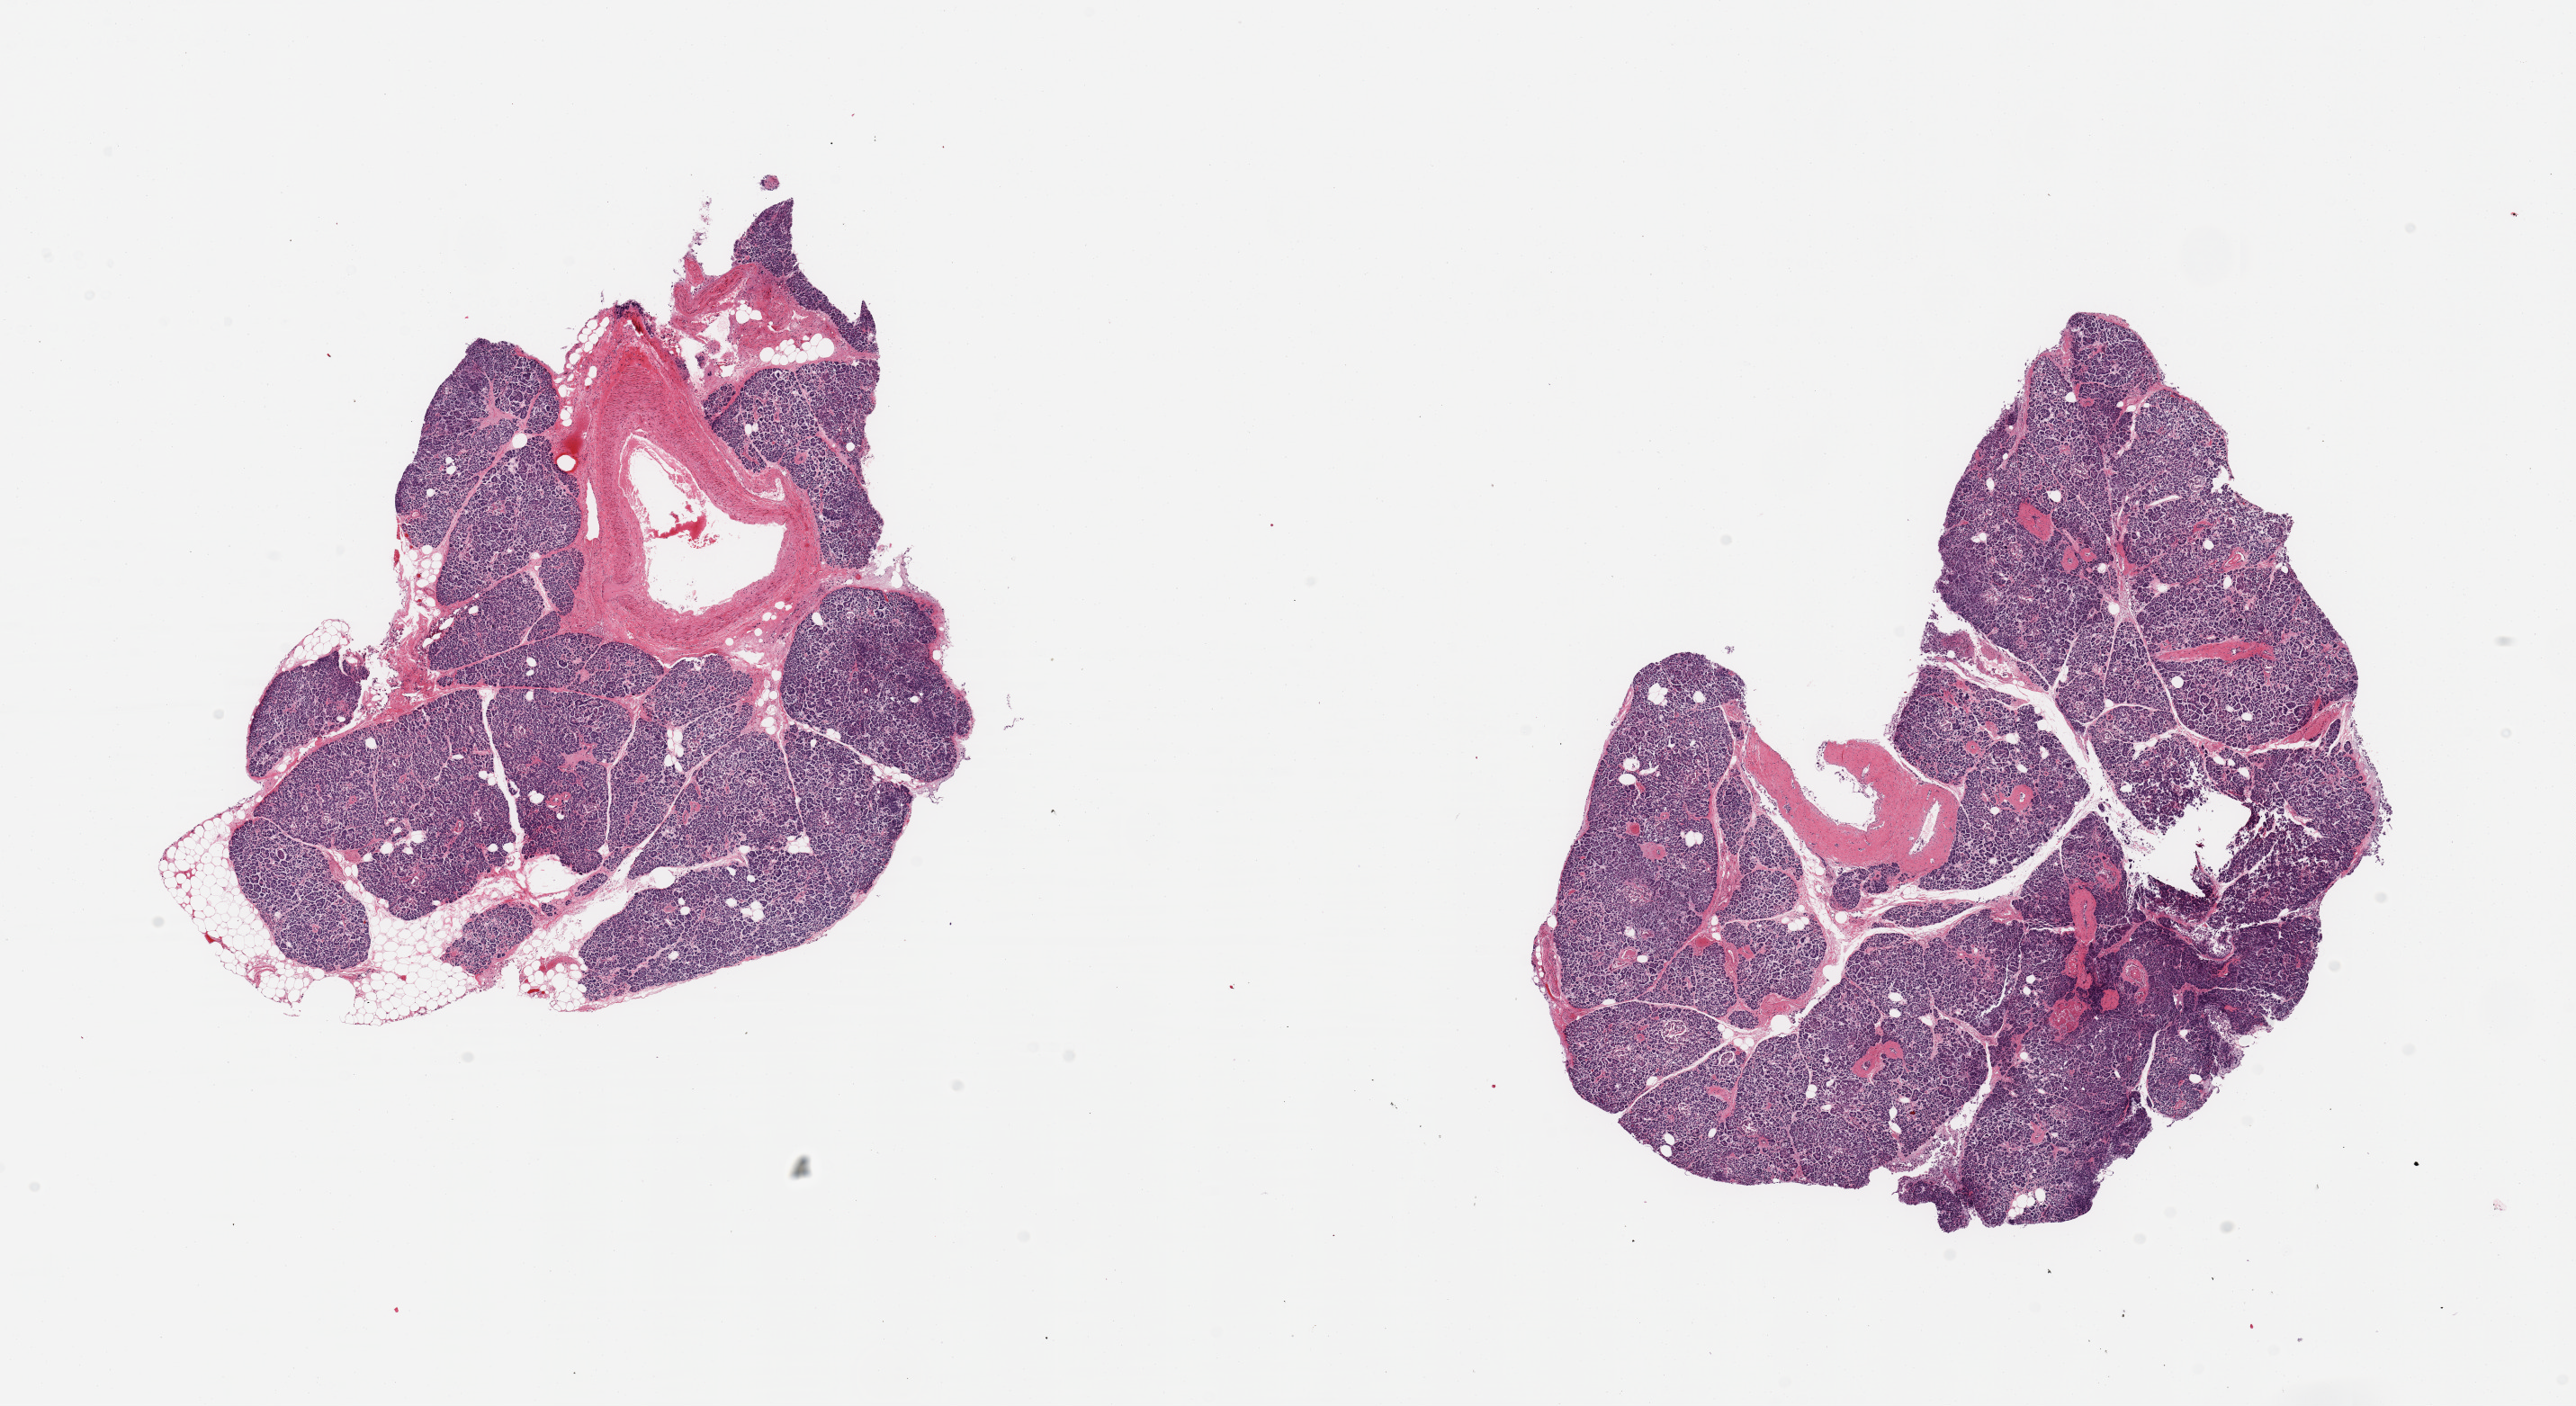
Digitized haematoxylin and eosin-stained section, whole scanned area (about 22.6 x 12.4 mm, from a 20x scan) shown as a low-resolution overview. PAXgene-fixed paraffin-embedded (PFPE) section. Target tissue: pancreas. Donor tissue sample. Donor: female.
Review note (as recorded): 2 pieces, moderately advanced saponificatino; some islets visible, moderately degraded.